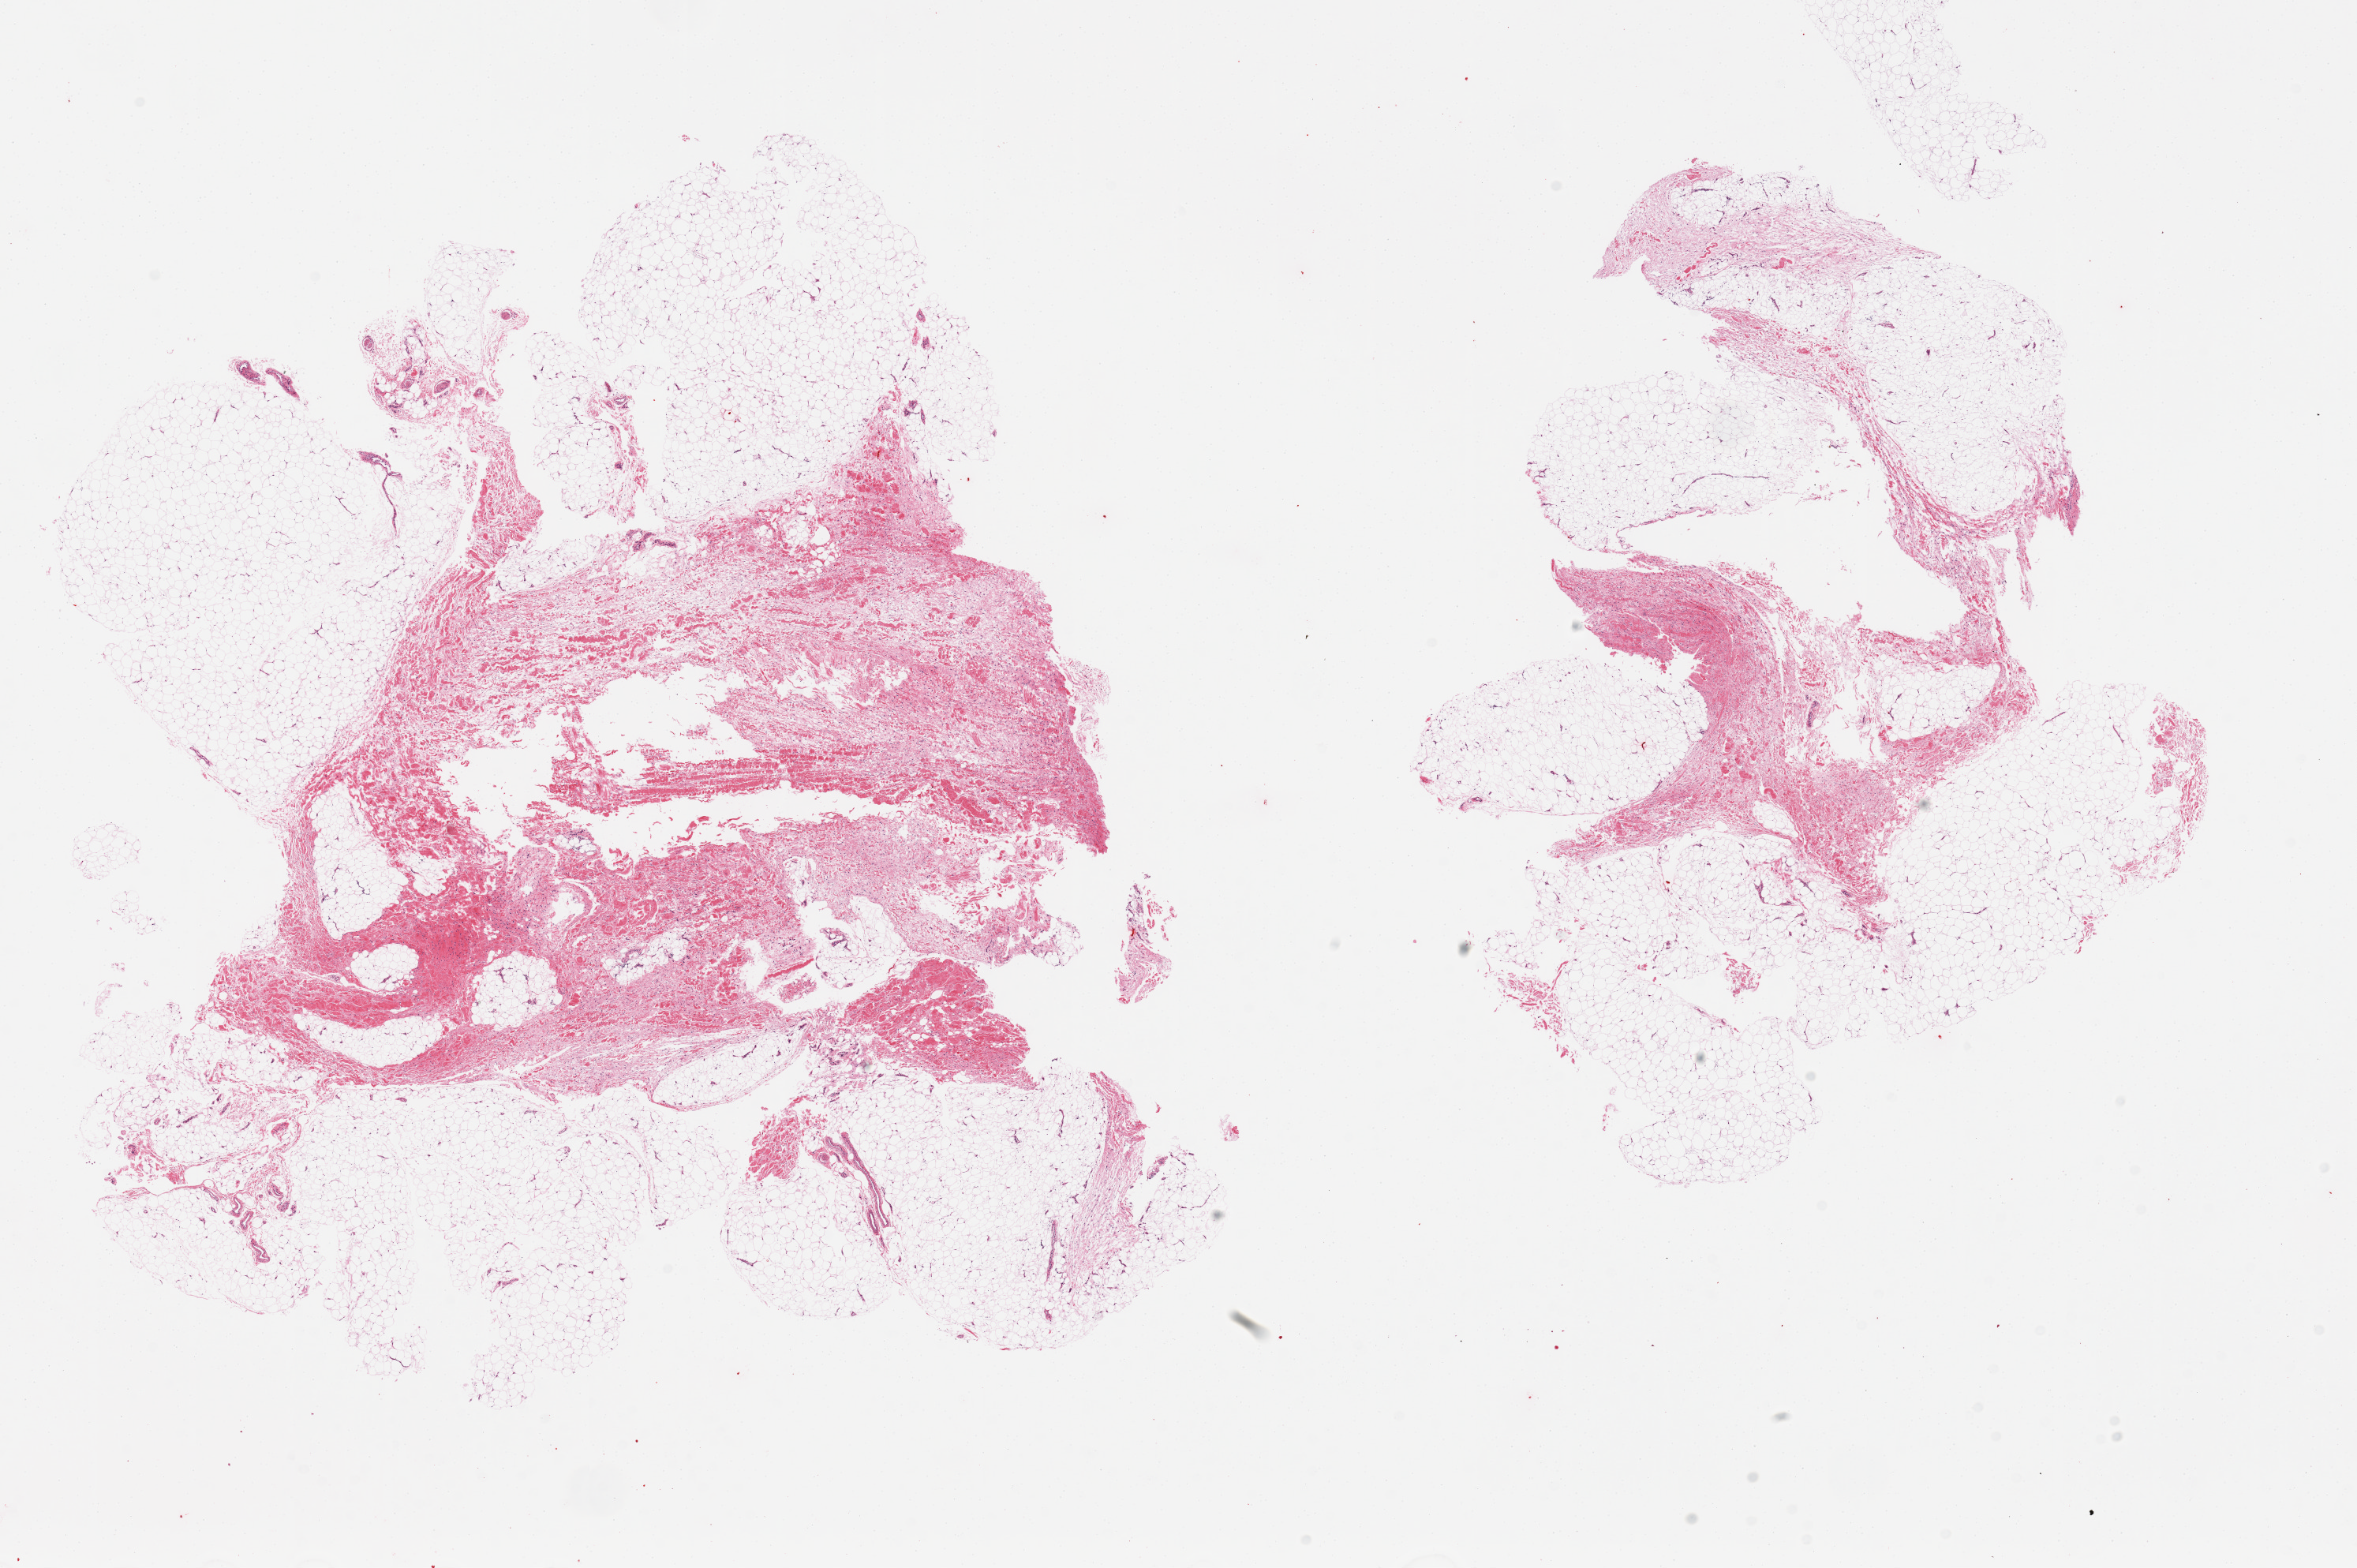
Hematoxylin and eosin (H&E) whole-slide image, shown as a low-resolution overview of the whole scanned area (about 23.6 x 15.7 mm), PAXgene-fixed paraffin-embedded (PFPE) section, target tissue: adipose tissue, donor tissue sample.
Pathologist's review note for this sample: 2 pieces: 1 50% fibrous content, other 20% fibrous.